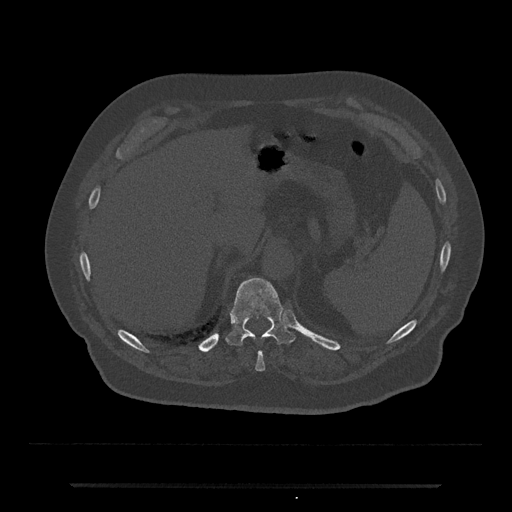
CT including the spine, one axial slice; slice 662 of 797 in the series (ordered by position); reconstruction kernel Br40s/3; 120 kVp; bone window (W 1800 / L 400 HU); 0.5 mm slice thickness; 512 × 512 image matrix, field of view 434 × 434 mm. Patient: male, 80 years. From the clinical record (not read from this slice): primary cancer: prostate.
Annotated regions visible in this slice (semi-automatically segmented with operator editing):
- T10 vertebra: bounding box [x1, y1, x2, y2] px = [255, 352, 265, 371]
- T11 vertebra: [226, 277, 295, 346]